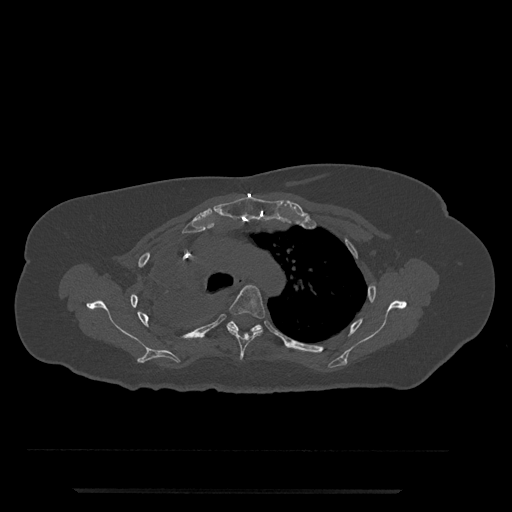
CT including the spine, one axial slice; reconstruction kernel Br40s/3; 120 kVp; bone window (W 1800 / L 400 HU); 0.5 mm slice thickness; 512 × 512 image matrix, field of view 440 × 440 mm. Female patient, age 51 years. From the clinical record (not read from this slice): primary cancer: neuro; vertebrae with lytic lesions (as recorded): T8.
Structures marked on this image (semi-automatic segmentation, software-assisted and operator-edited):
- T4 vertebra: bounding box <210,285,265,360> (left, top, right, bottom; pixels)
- T5 vertebra: <227,321,276,335>